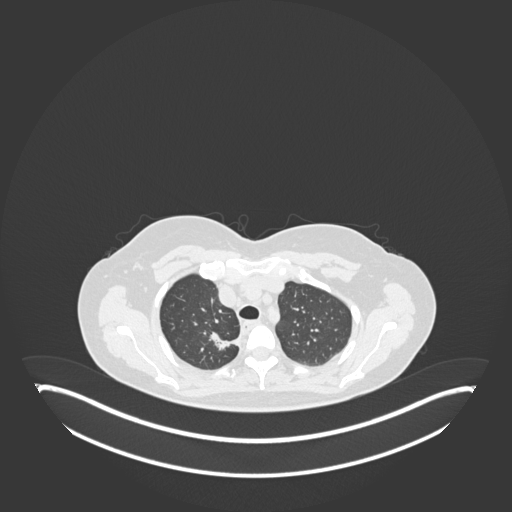
Chest CT, one axial slice. Position 142 of 181 along the scan axis. Reconstruction kernel B30f. Lung window (W 1500 / L -600 HU). 1 mm slice thickness. 512 × 512 image matrix, field of view 500 × 500 mm. Patient: female, 65 years. Case-level facts recorded for this patient, not image findings: clinical TNM (as recorded): T1b N0 M0.
Structures marked on this image (rectangle marked by the reading radiologist):
- lung tumour (recorded histology: adenocarcinoma): box from (x=205, y=327) to (x=240, y=350) px